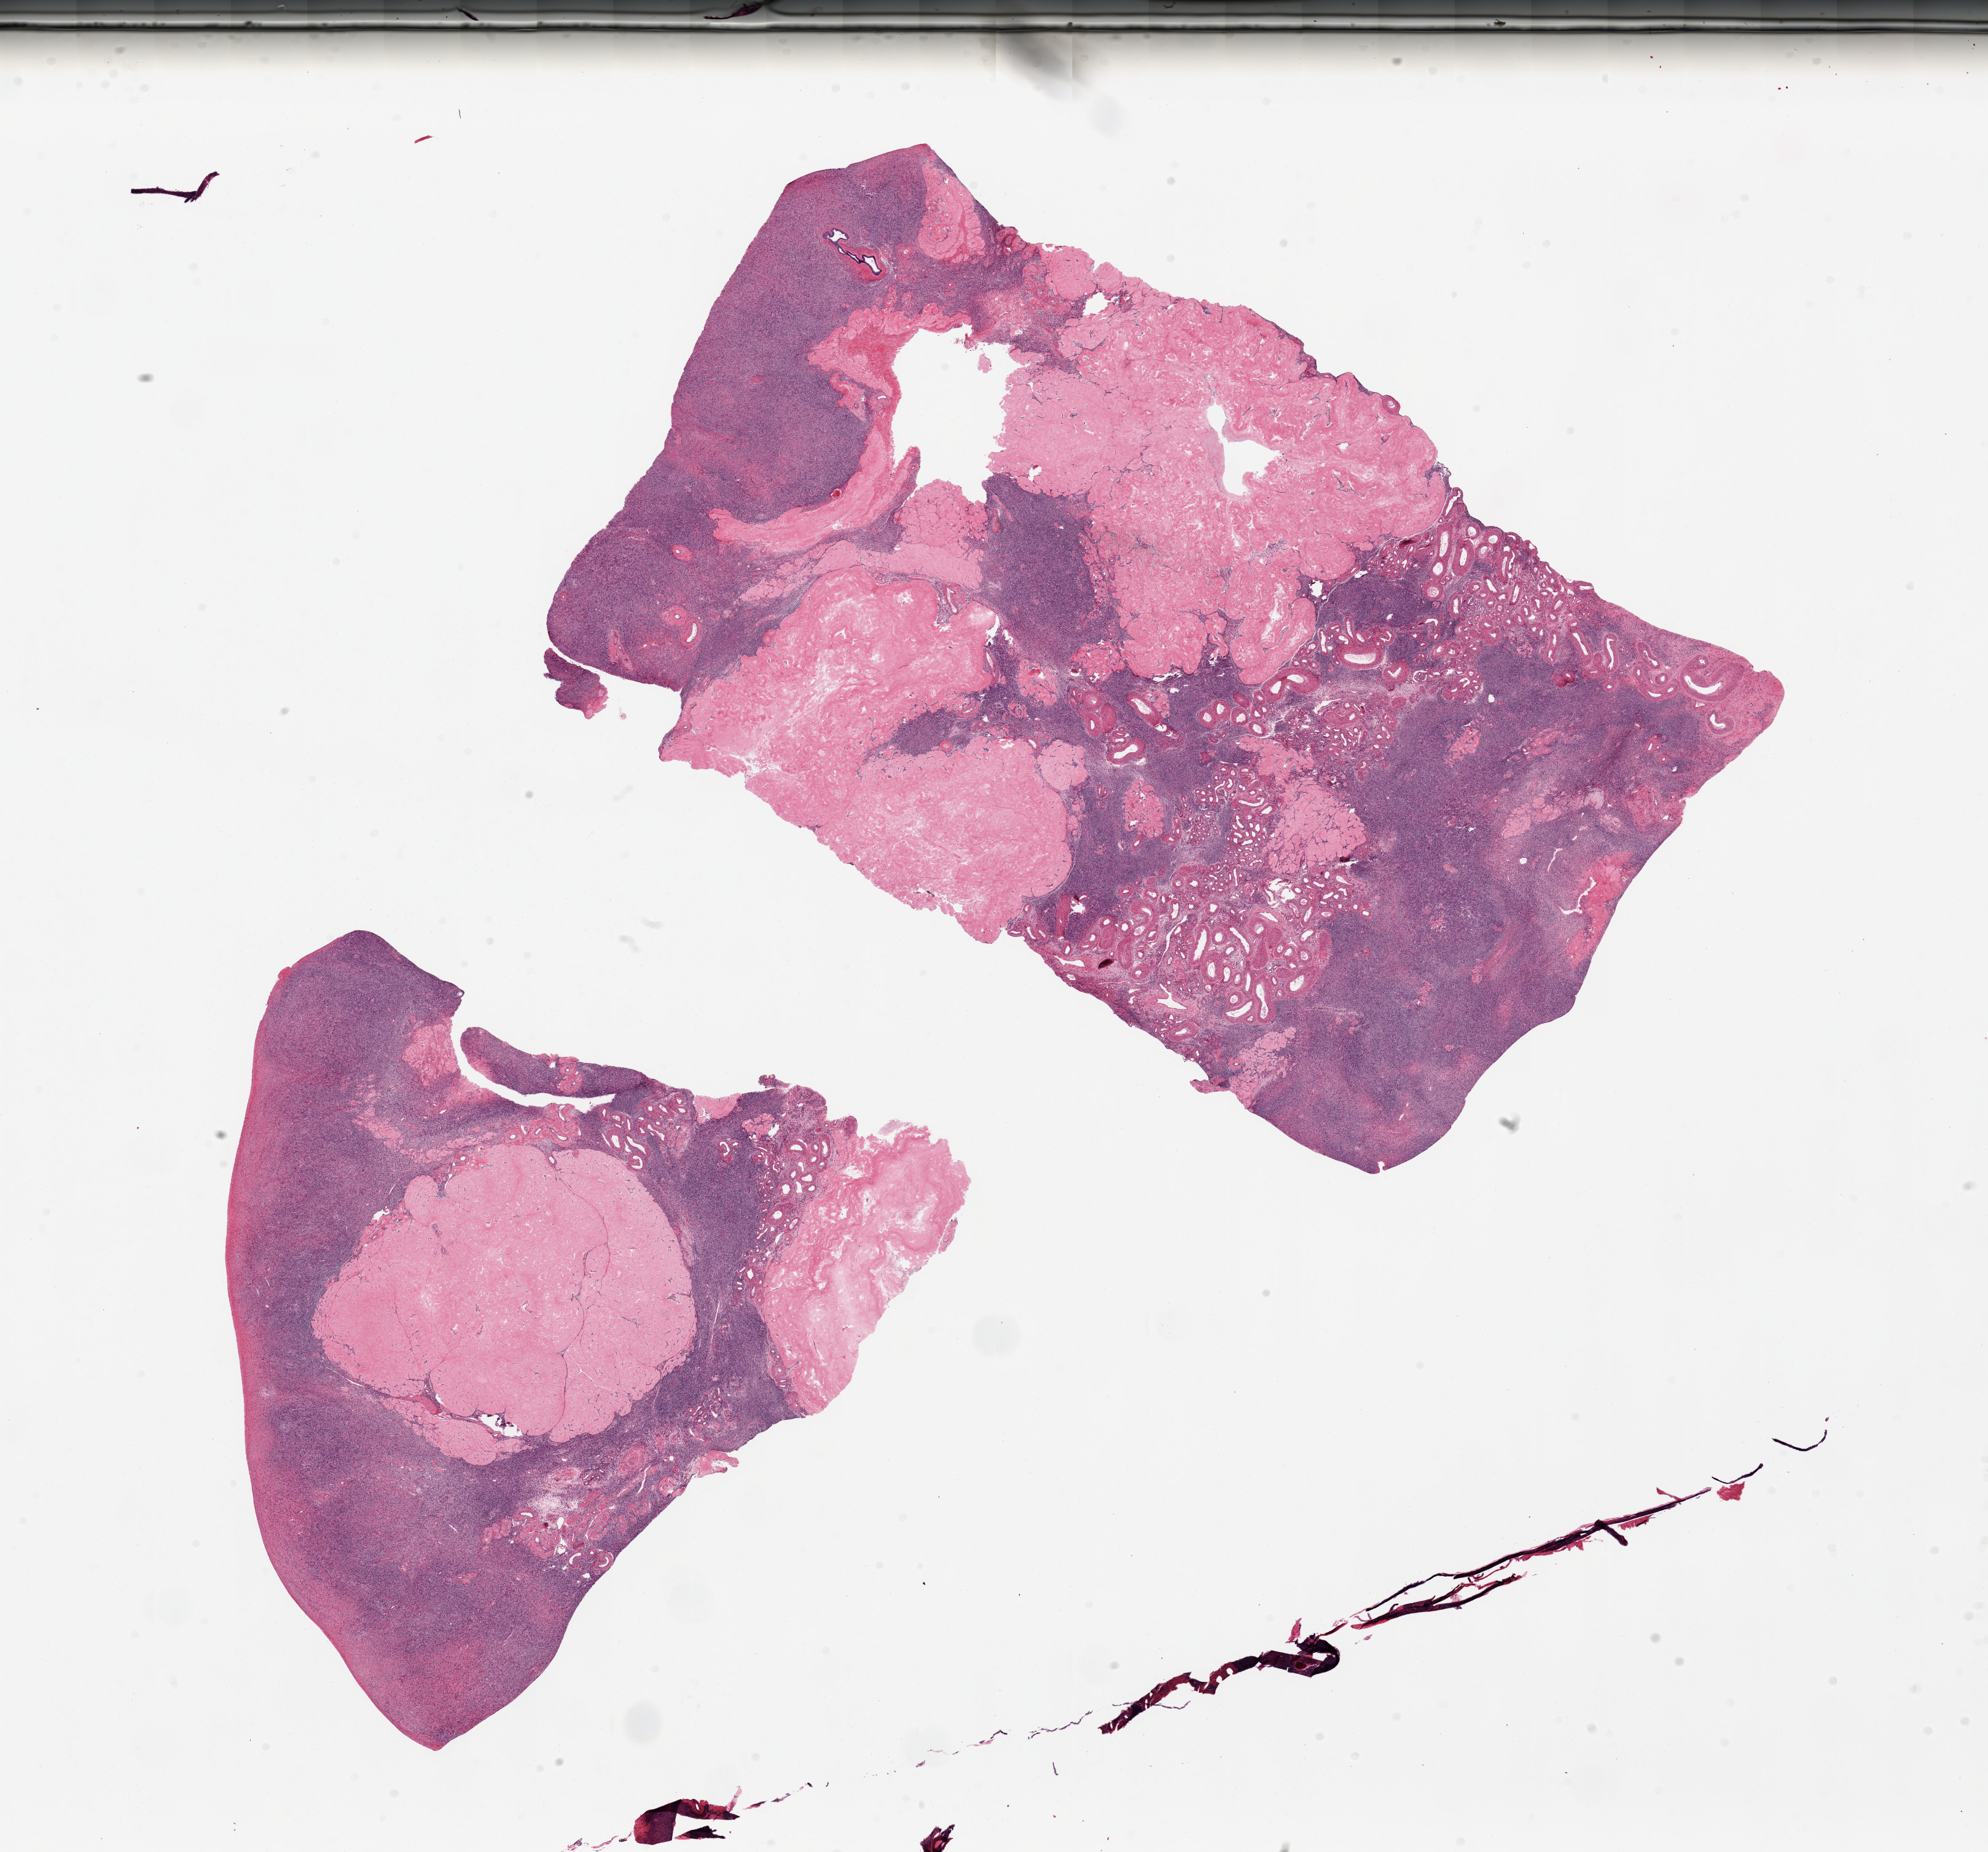
Whole-slide image, hematoxylin and eosin (H&E) stain — shown as a low-resolution overview of the whole scanned area (about 25.6 x 23.8 mm), PAXgene-fixed paraffin-embedded (PFPE) section, sampled site (target tissue): ovary, donor tissue sample. Donor: female.
Reviewer comment on this tissue sample: 2 pieces, 10x10 & 14x9mm; nmerous coropora albicanita.